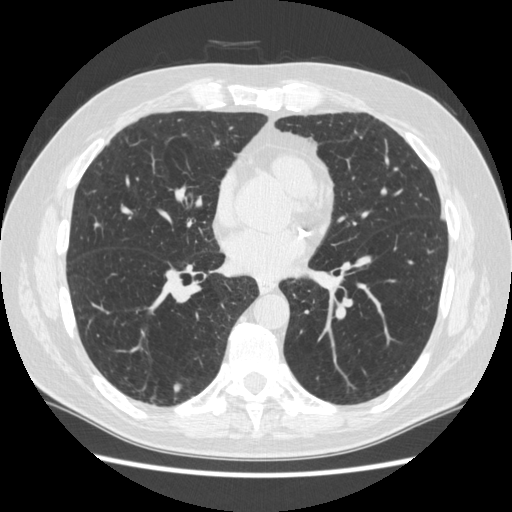
Low-dose screening chest CT, one axial slice; reconstruction kernel STANDARD; 120 kVp; lung window (W 1500 / L -600 HU); 1.25 mm slice thickness; 512 × 512 image matrix, field of view 360 × 360 mm.
Outlined on this slice (expert manual segmentation):
- lesion 3 (nodule, lower lobe of right lung): box from (x=174, y=383) to (x=182, y=391) px